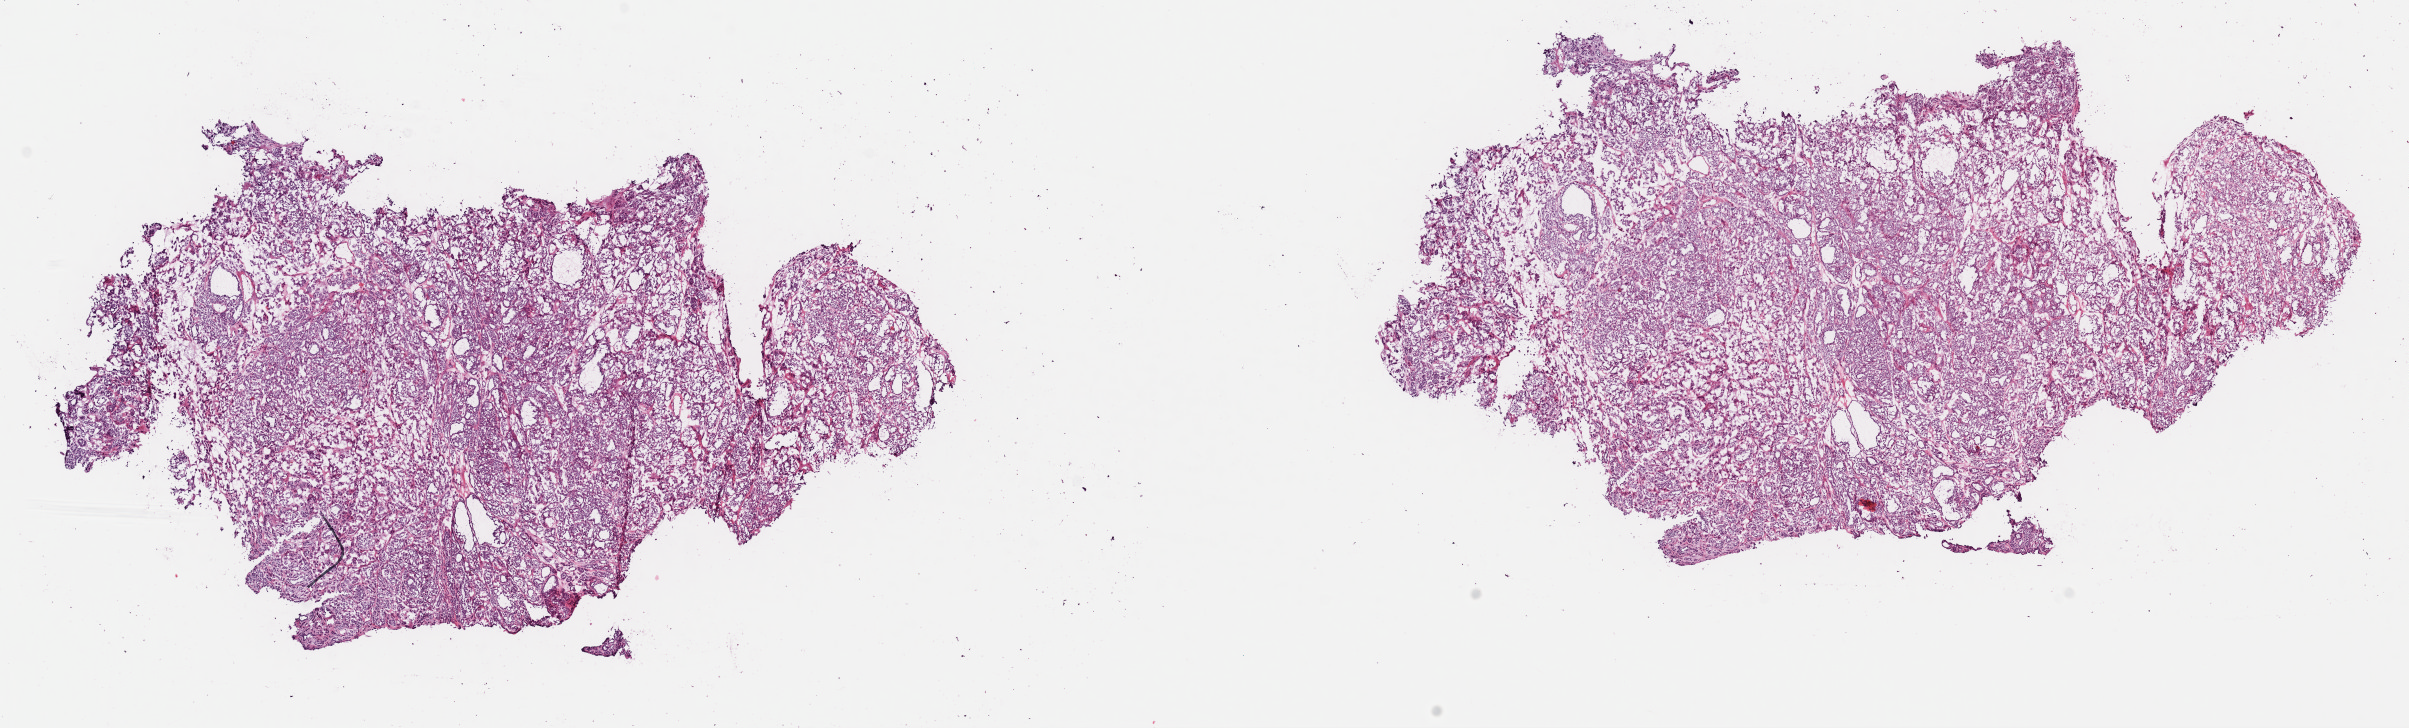
H&E-stained whole-slide image, low-resolution overview of the scanned area, about 19.0 x 5.8 mm; frozen section from the top of the tissue portion; primary tumour sample from the thyroid. Patient: female, age at initial diagnosis 44 years. Slide review estimates, as recorded: tumour cells 85%, tumour nuclei 85%, normal cells 0%, stromal cells 15%, necrosis 0%. Infiltration values recorded for this section: lymphocyte infiltration 1%, monocyte infiltration 0%, neutrophil infiltration 0%.
Histologic diagnosis: Papillary carcinoma, follicular variant (thyroid gland). AJCC pathologic stage: I (7th edition). TNM: T2 NX MX.